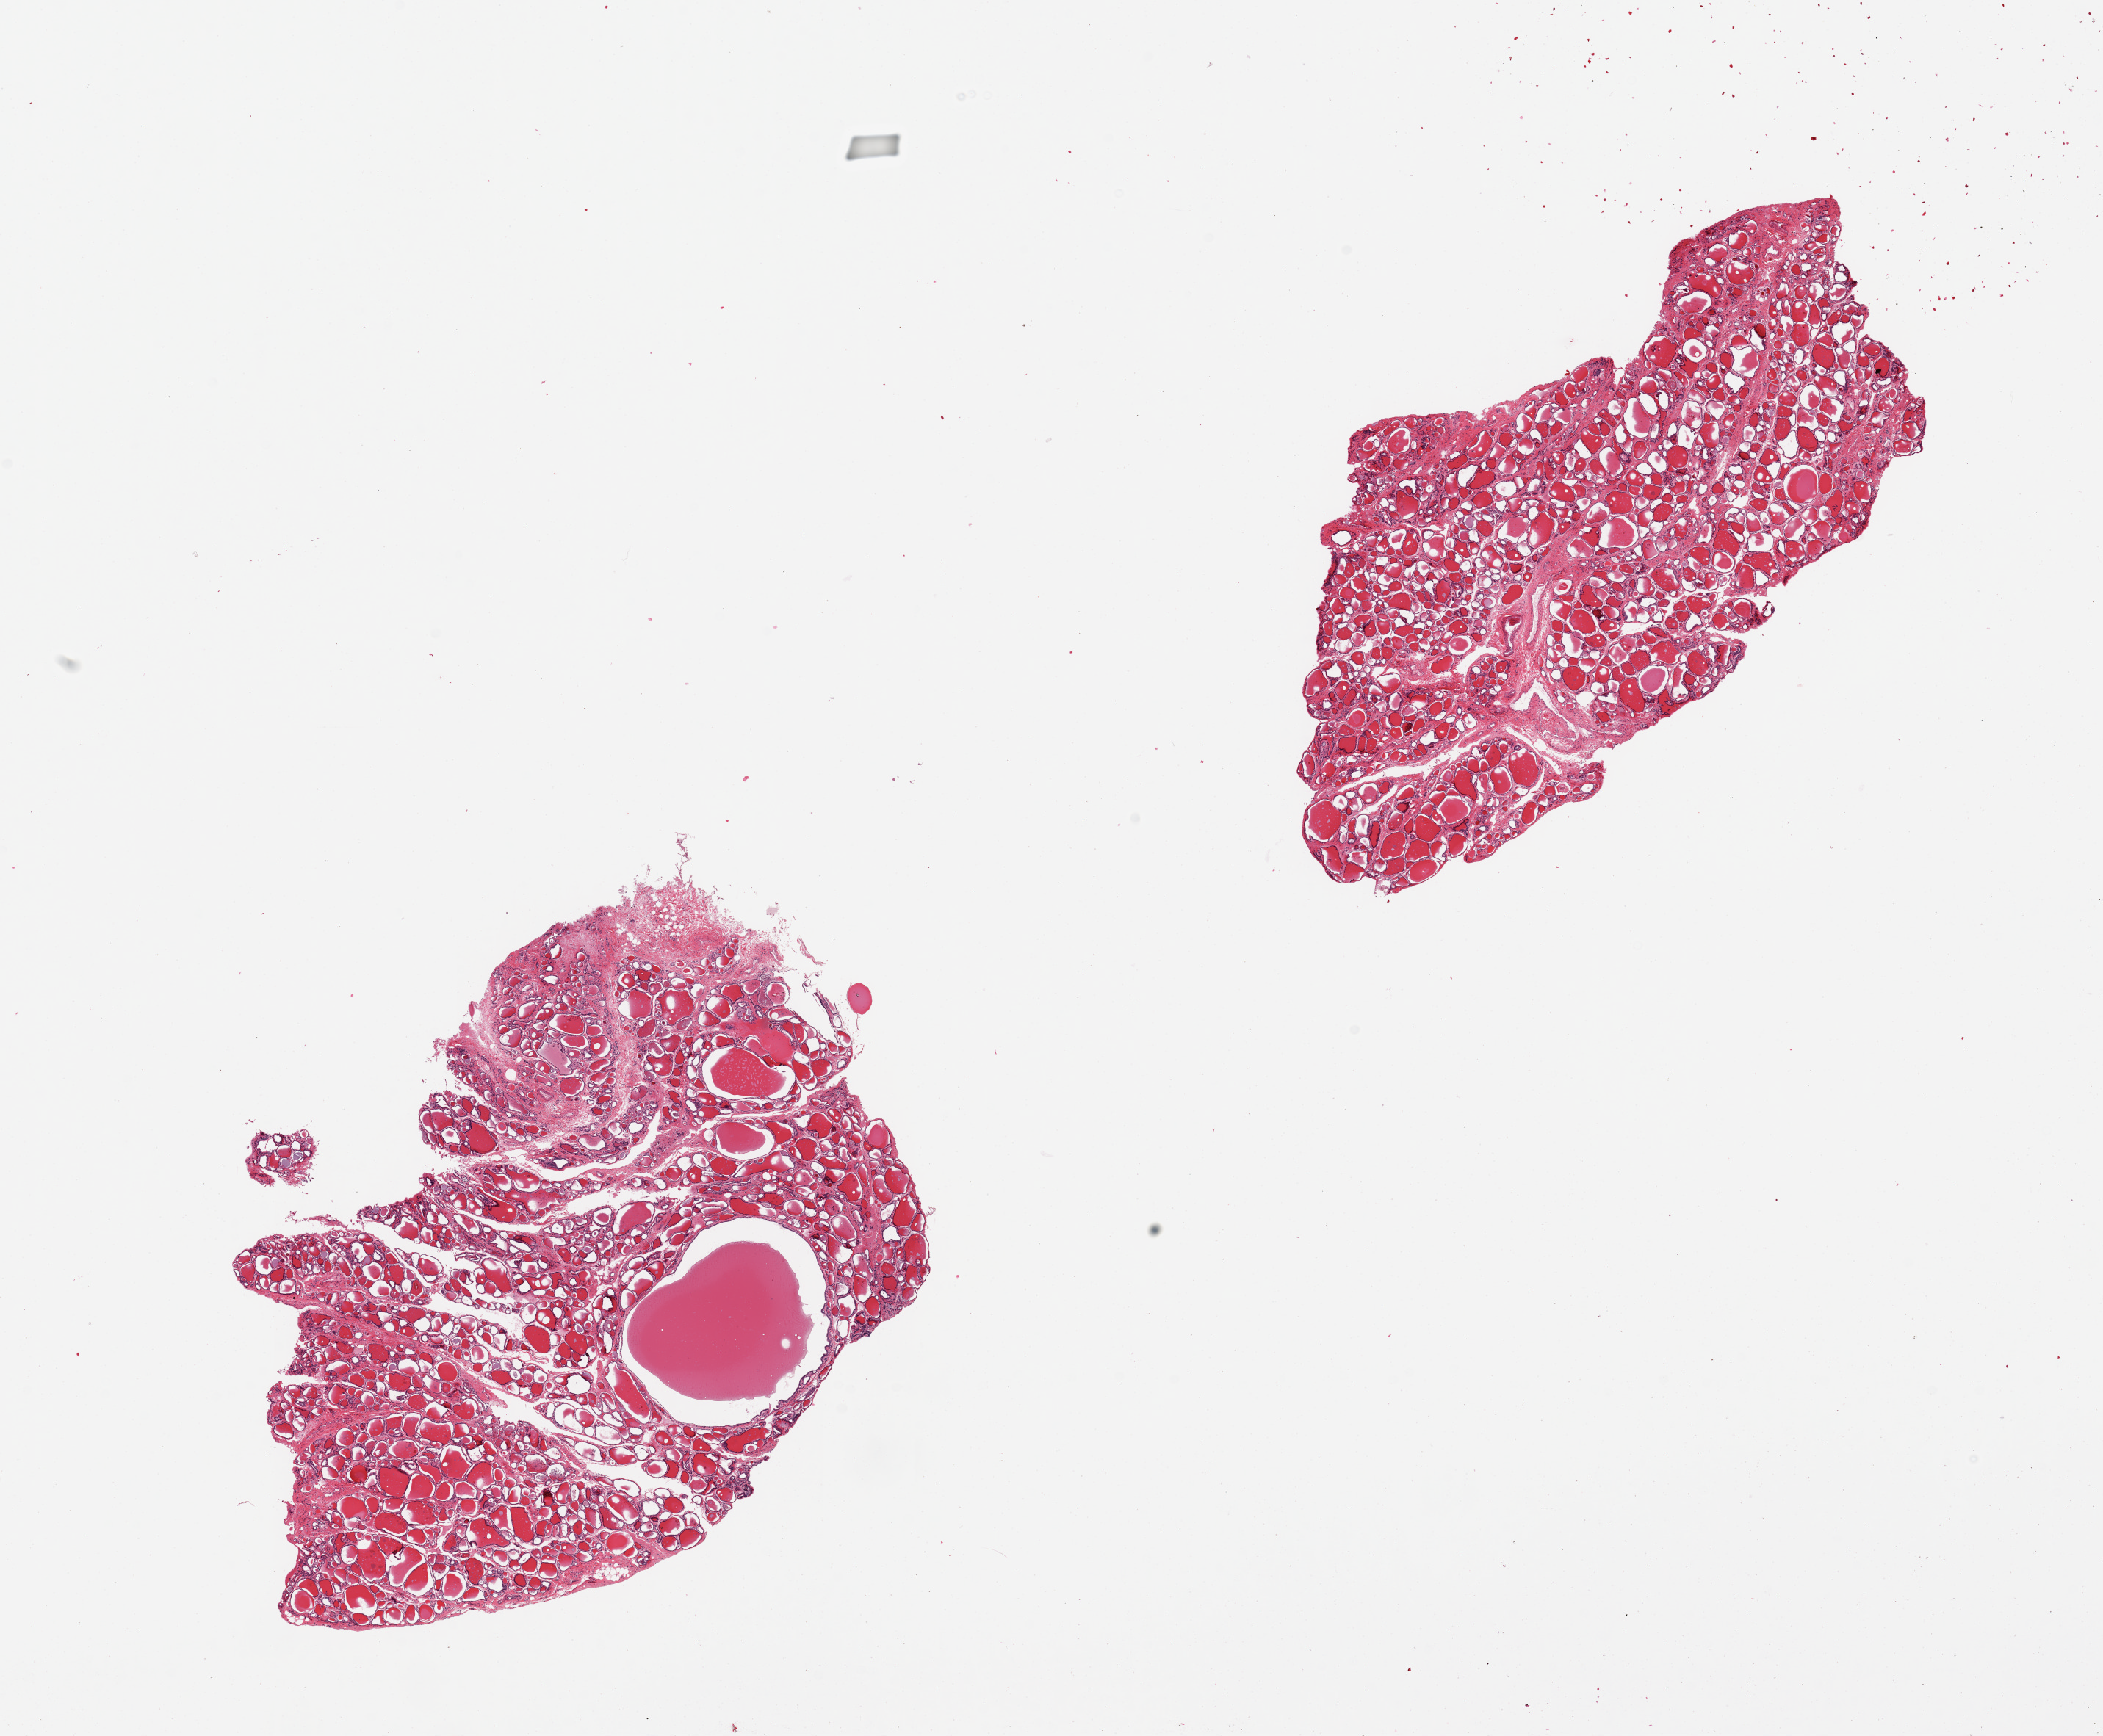
H&E whole-slide image — whole scanned area (about 22.6 x 18.7 mm) shown as a low-resolution overview; PAXgene-fixed paraffin-embedded (PFPE) section; section of thyroid (target tissue); donor tissue sample.
Reviewer comment on this tissue sample: 2 pieces, 2mm colloid cyst; Mild generalized goiter with regressive changes.